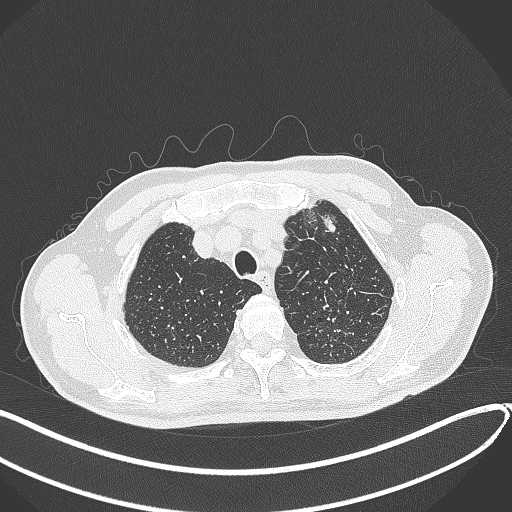
Chest CT, one axial slice. Slice 356 of 459 in the series (ordered by position). 120 kVp. Lung window (W 1500 / L -600 HU). 1 mm slice thickness. 512 × 512 image matrix. Patient: male, 74 years. From the clinical record (not read from this slice): clinical TNM (as recorded): T2b N0 M1c.
Outlined on this slice (bounding box drawn by a radiologist):
- lung tumour (recorded histology: adenocarcinoma): bounding box <319,210,338,235> (left, top, right, bottom; pixels)